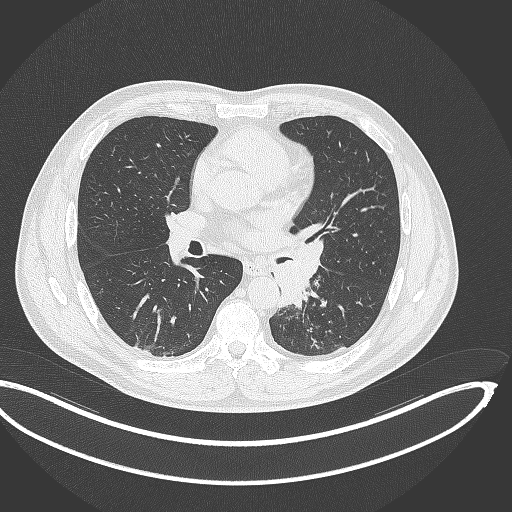
Chest CT, one axial slice. Position 187 of 362 along the scan axis. Lung window (W 1500 / L -600 HU). 512 × 512 image matrix. Male patient, age 50 years. Case-level facts recorded for this patient, not image findings: clinical TNM (as recorded): T2a N3 M0.
Annotated regions visible in this slice (bounding box drawn by a radiologist):
- lung tumour (recorded histology: squamous cell carcinoma): bounding box [x1, y1, x2, y2] px = [264, 233, 327, 309]